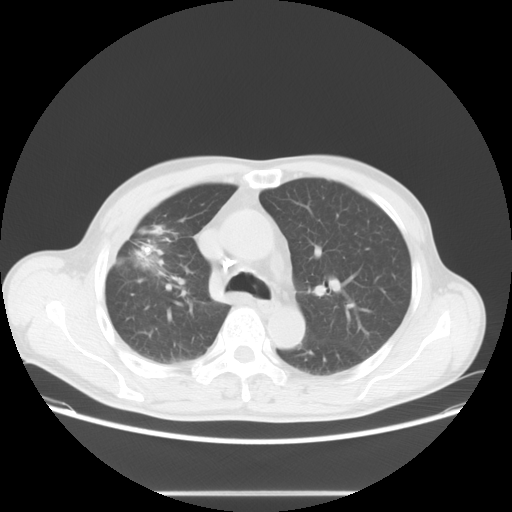
Chest CT, one axial slice; slice 46 of 69 in the series (ordered by position); reconstruction kernel STANDARD; lung window (W 1500 / L -600 HU); 5 mm slice thickness; 512 × 512 image matrix, field of view 392 × 392 mm. Patient: male, 67 years. From the clinical record (not read from this slice): clinical TNM (as recorded): T2 N0 M0.
Outlined on this slice (bounding box drawn by a radiologist):
- lung tumour (recorded histology: adenocarcinoma): bounding box (x1, y1, x2, y2) in pixels: (128, 241, 160, 265)